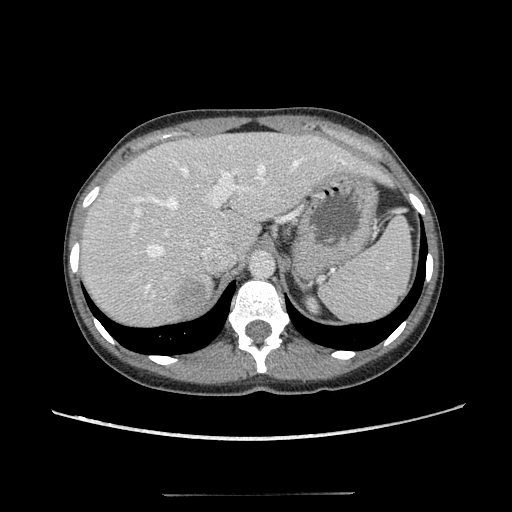
Contrast-enhanced abdominal CT, one axial slice. Slice 84 of 117 in the series (ordered by position). Reconstruction kernel STANDARD. 120 kVp. Soft-tissue window (W 400 / L 40 HU). 2.5 mm slice thickness. 512 × 512 image matrix. Female patient, age 35 years. Case-level facts recorded for this patient, not image findings: diagnosis: adrenocortical carcinoma; tumour side: right adrenal; tumour size at pathology: 3 cm; Ki-67 index: 21 %; stage (as recorded): 3.
Structures marked on this image (semi-automatically segmented with operator editing):
- mass: bounding box [x1, y1, x2, y2] px = [175, 280, 205, 314]